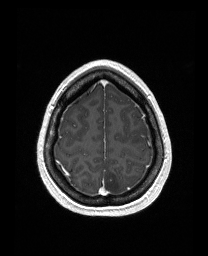
Brain MRI from a brain-tumour surgery series, one axial slice. Slice 132 of 176 in the series (ordered by position). T1-weighted post-contrast. 1 mm slice thickness. 208 × 256 image matrix. Case-level facts recorded for this patient, not image findings: histopathology: Astrocytoma; WHO grade: 3; IDH mutation: yes.
Annotated regions visible in this slice (expert manual segmentation):
- tumour: bounding box [x1, y1, x2, y2] px = [131, 126, 150, 146]